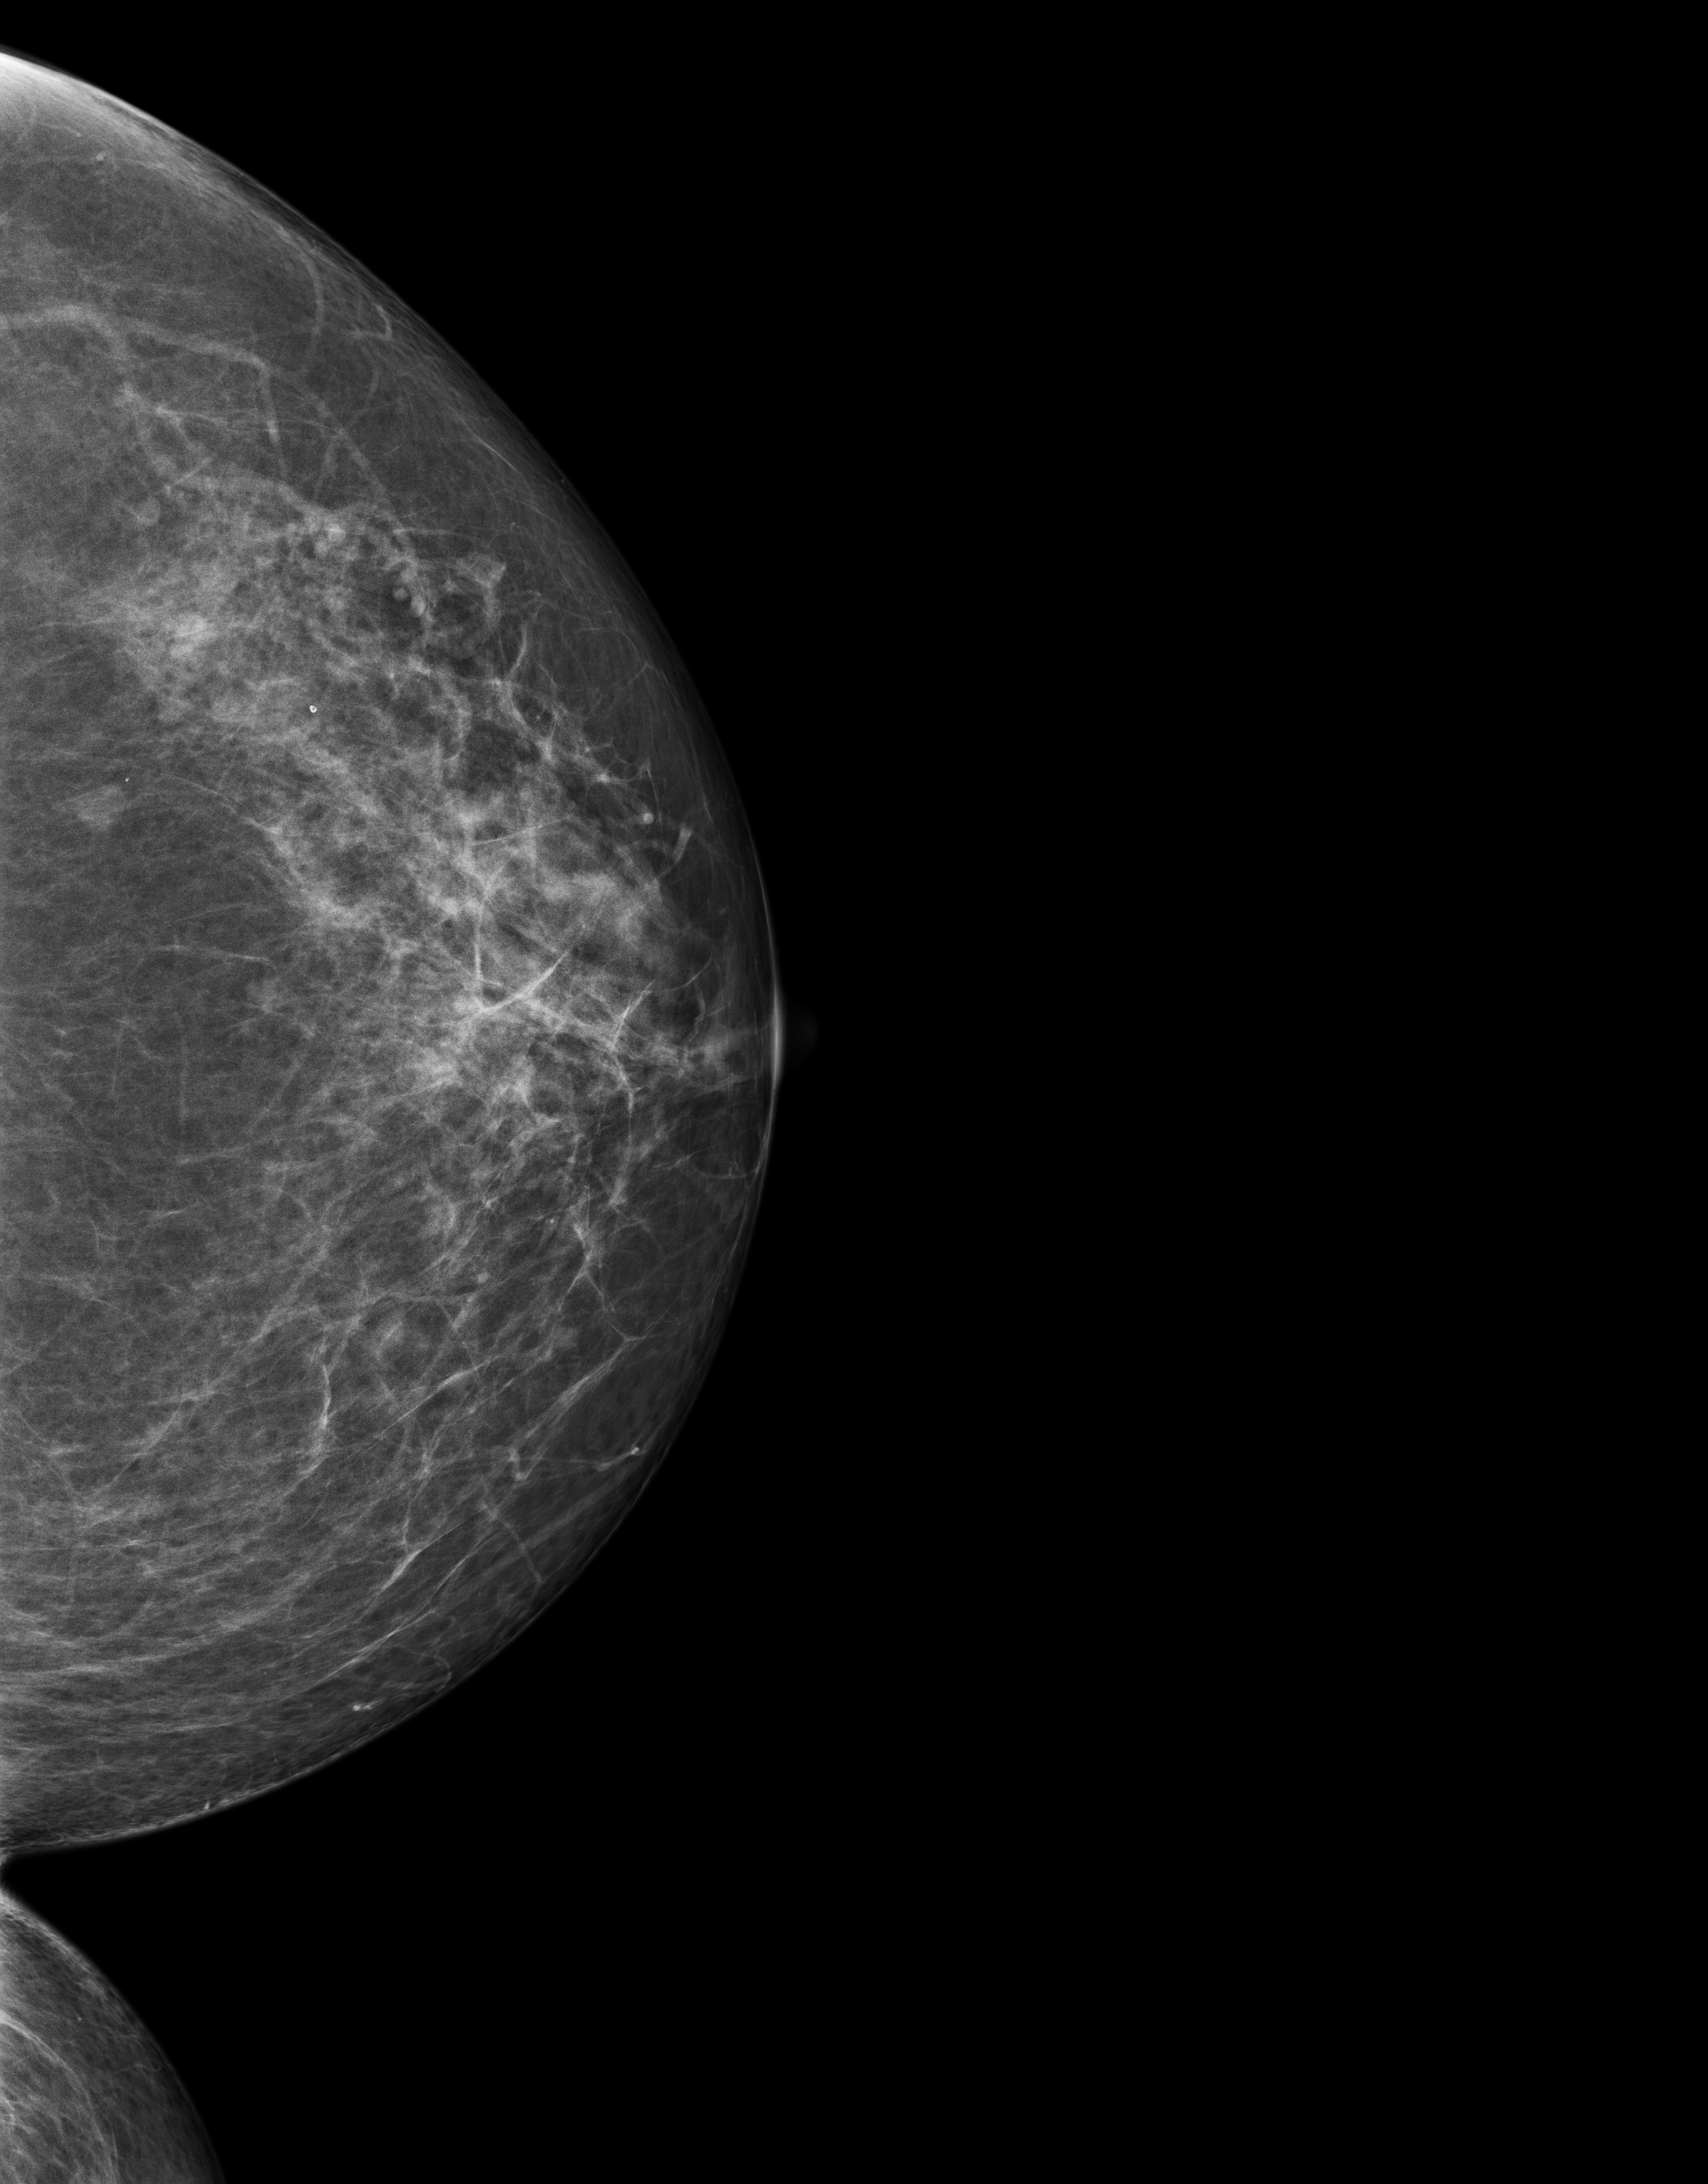
Full-field digital mammogram (FFDM); left breast; CC view; screening examination. Female patient, age 53 years.
BI-RADS breast density category at the screening exam (both breasts, scale 1–4): 3. Final BI-RADS assessment for this screening round (tomosynthesis exam, both breasts): category 4. Recall: recalled for additional imaging after this screen.